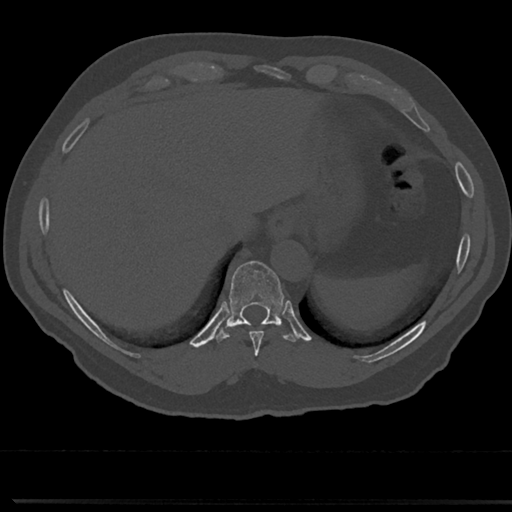
CT including the spine, one axial slice. Position 274 of 817 along the scan axis. 120 kVp. Bone window (W 1800 / L 400 HU). 0.5 mm slice thickness. 512 × 512 image matrix, field of view 355 × 355 mm. Patient: male, 61 years. Case-level facts recorded for this patient, not image findings: primary cancer: prostate.
Outlined on this slice (semi-automatically segmented with operator editing):
- T10 vertebra: box from (x=230, y=261) to (x=283, y=323) px
- T8 vertebra: (x=237, y=302)–(x=281, y=368)
- T9 vertebra: (x=228, y=291)–(x=286, y=349)